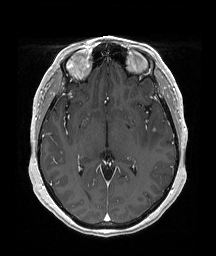
Brain MRI from a brain-tumour surgery series, one axial slice. Slice 107 of 192 in the series (ordered by position). T1-weighted post-contrast. 1 mm slice thickness. 216 × 256 image matrix, field of view 211 × 250 mm. Case-level facts recorded for this patient, not image findings: histopathology: Papillary glioneuronal tumor; WHO grade: 1; tumour location: Left Temporal.
Annotated regions visible in this slice (expert manual segmentation):
- tumour: bounding box <151,127,155,131> (left, top, right, bottom; pixels)